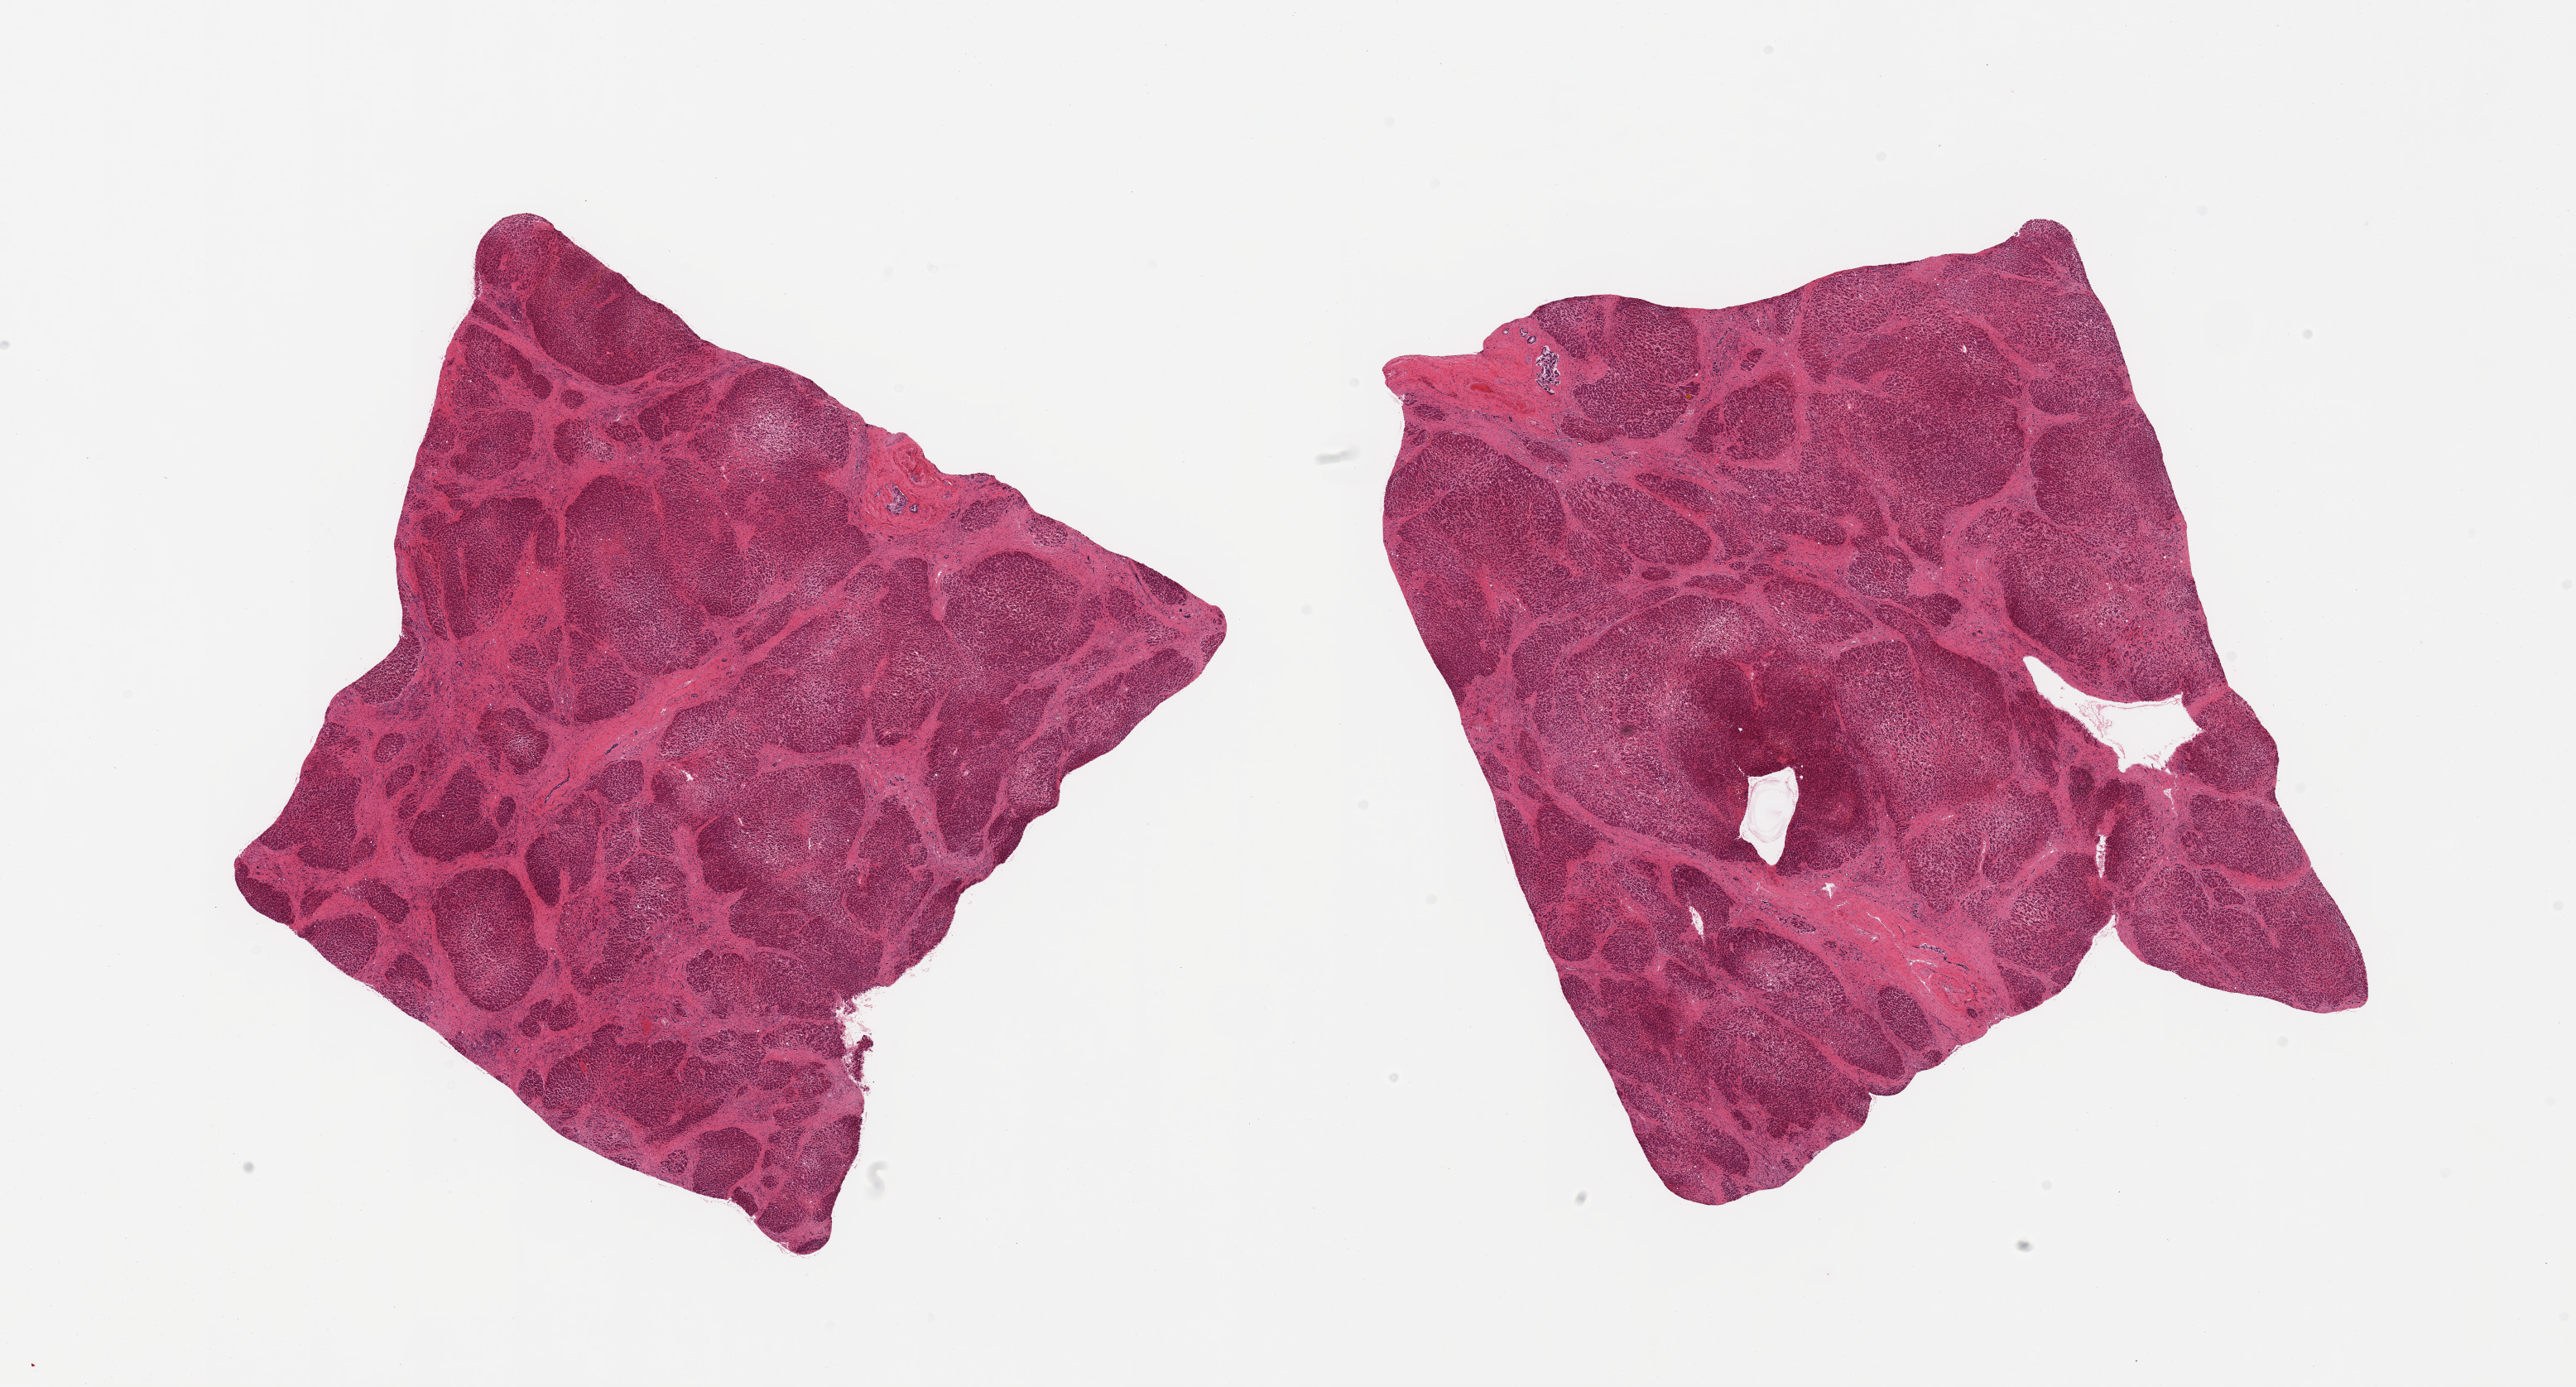
Whole-slide image, haematoxylin and eosin stain, brightfield, whole scanned area (about 24.6 x 13.2 mm) shown as a low-resolution overview. PAXgene-fixed, paraffin-embedded tissue. Section of liver (target tissue). Donor tissue sample. Female donor.
Pathologist's review note for this sample: 2 pieces; nodular cirrhosis.